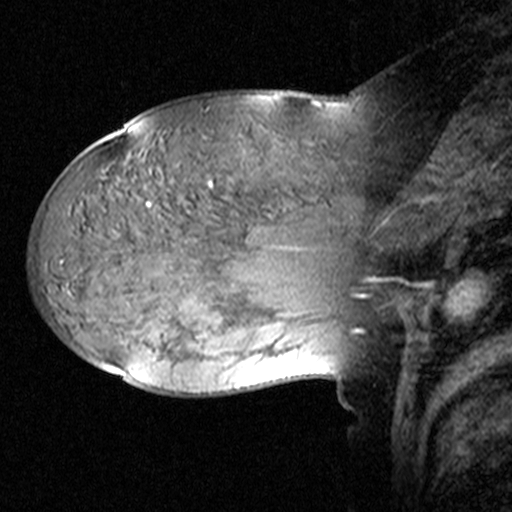
Breast MRI (dynamic contrast-enhanced), one sagittal slice. Slice 27 of 44 in the series (ordered by position). Dynamic contrast-enhanced study with each time point stored as its own series, time point 2 of 3 at this slice position (early post-contrast, ordered by acquisition time). 1.5 T. TE 4.5 ms, TR 11 ms. 3 mm slice thickness. 512 × 512 image matrix, field of view 240 × 240 mm. Female patient, age 38 years. From the clinical record (not read from this slice): setting: breast cancer imaged before/during neoadjuvant chemotherapy; receptor status: HR-positive, HER2-negative.
Annotated regions visible in this slice (semi-automatic segmentation, software-assisted and operator-edited):
- analysis volume of interest (the breast-tissue region the enhancement analysis was run in; not a lesion): bounding box [x1, y1, x2, y2] px = [124, 106, 405, 245]
- tumour enhancement mask (voxels above the 90 % enhancement threshold inside the analysis volume of interest): [147, 202, 151, 207]